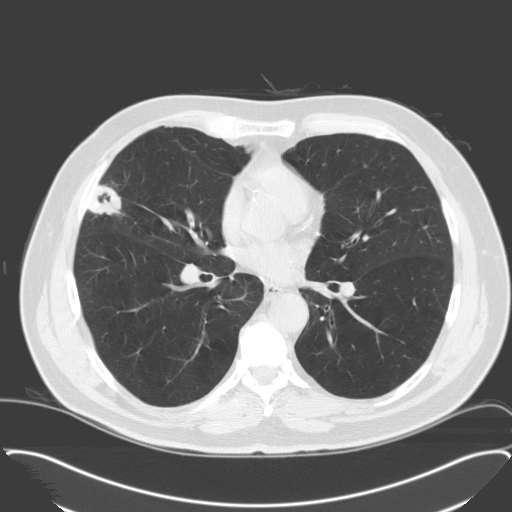
Low-dose screening chest CT, axial slice; third screening round (two years after baseline); lung window (W 1500 / L -600 HU); standard (soft-tissue) reconstruction kernel (C); slice 85 of 174 in the series; 512 × 512 image matrix, field of view 400 × 400 mm. Male participant, aged 65 years at enrolment. Former smoker at enrolment.
Expert-annotated lung lesion, bounding box (x1, y1, x2, y2) in pixels: (71, 179, 130, 233). The exam's reader record, not a measurement of the box and not confirmed to be the same lesion: non-calcified nodule or mass ≥4 mm, right middle lobe, 28 × 23 mm, spiculated (stellate) margins, soft tissue attenuation, pre-existing on the prior screen: no. Participant outcome: lung cancer diagnosed 25 days after this screen — adenocarcinoma, NOS, right middle lobe, moderately differentiated (G2), stage IA (AJCC 6th edition), 25 mm at pathology.